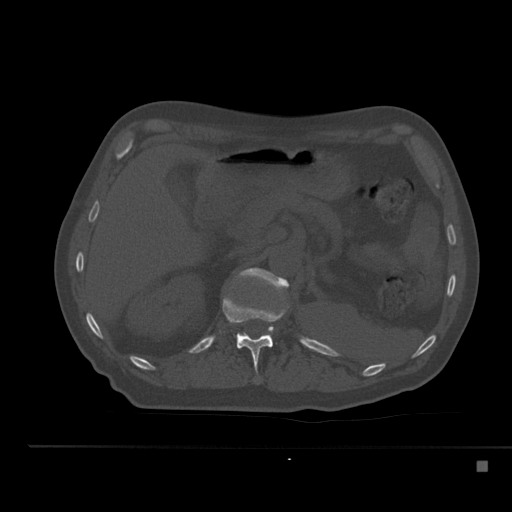
CT including the spine, one axial slice. Position 224 of 517 along the scan axis. Reconstruction kernel Br40s. 120 kVp. Bone window (W 1800 / L 400 HU). 1.5 mm slice thickness. 512 × 512 image matrix. Patient: male, 70 years. From the clinical record (not read from this slice): primary cancer: renal; vertebrae with lytic lesions (as recorded): T4, T6, T10, T12, L3, L4, L5.
Outlined on this slice (semi-automatically segmented with operator editing):
- L1 vertebra: bounding box [x1, y1, x2, y2] px = [238, 268, 289, 333]
- T12 vertebra: [222, 296, 288, 371]